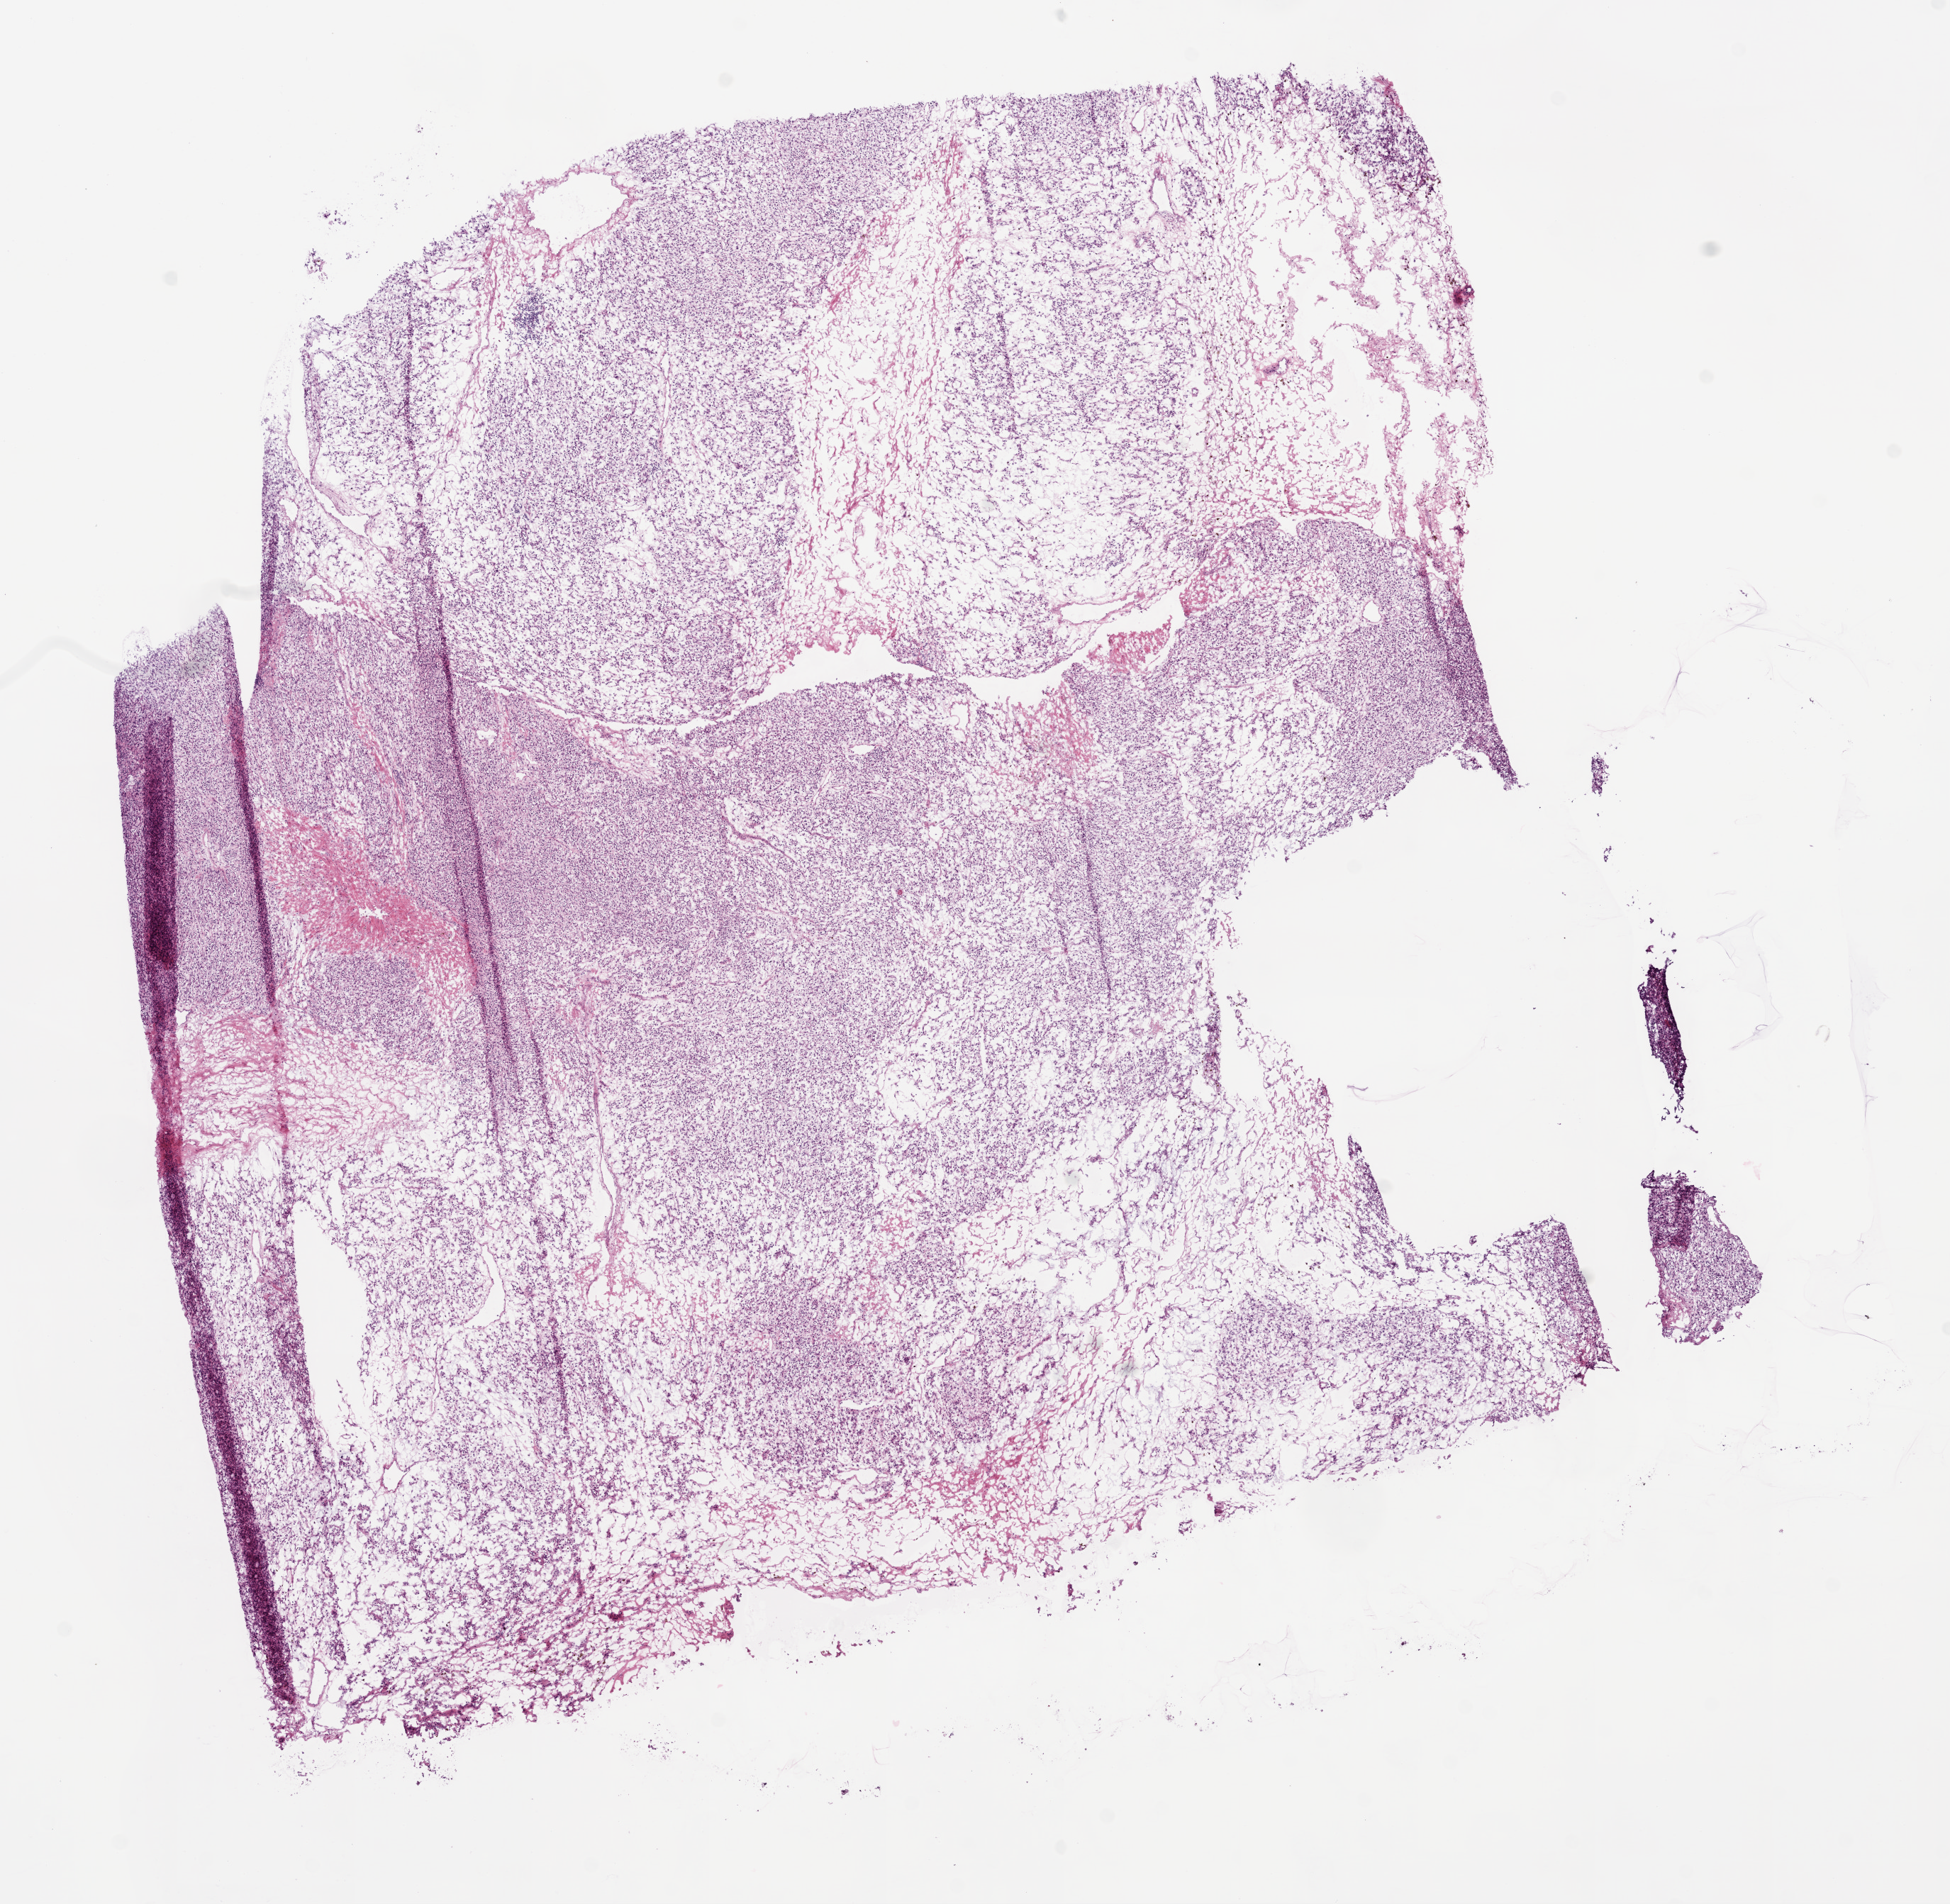
Digitized Hematoxylin and eosin (H&E) stained tissue section (whole slide), whole scanned area (about 11.0 x 10.8 mm, slide scanned at 20x) shown as a low-resolution overview, frozen section from the bottom of the tissue portion, sample: primary tumour, kidney. Male, age 51 years at initial diagnosis. Histologic grade: G2 (moderately differentiated). Slide review estimates, as recorded: tumour cells 90%, tumour nuclei 80%, normal cells 0%, stromal cells 10%, necrosis 0%.
Pathologic diagnosis: Clear cell adenocarcinoma, NOS. TNM: T1a N0 M0. AJCC pathologic stage: I.